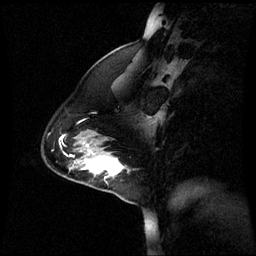
Breast MRI (dynamic contrast-enhanced), one sagittal slice; position 18 of 60 along the scan axis; dynamic contrast-enhanced series, image 2 of 3 at this slice position (ordered by acquisition); 1.5 T; TE 4.2 ms, TR 8.9 ms; 2.2 mm slice thickness; 256 × 256 image matrix, field of view 240 × 240 mm. Patient: female, 44 years. Case-level facts recorded for this patient, not image findings: setting: breast cancer imaged before/during neoadjuvant chemotherapy; receptor status: triple-negative.
Structures marked on this image (semi-automatic segmentation, software-assisted and operator-edited):
- analysis volume of interest (the breast-tissue region the enhancement analysis was run in; not a lesion): bounding box [x1, y1, x2, y2] px = [76, 150, 129, 185]
- tumour enhancement mask (voxels above the 70 % enhancement threshold inside the analysis volume of interest): [85, 158, 124, 175]